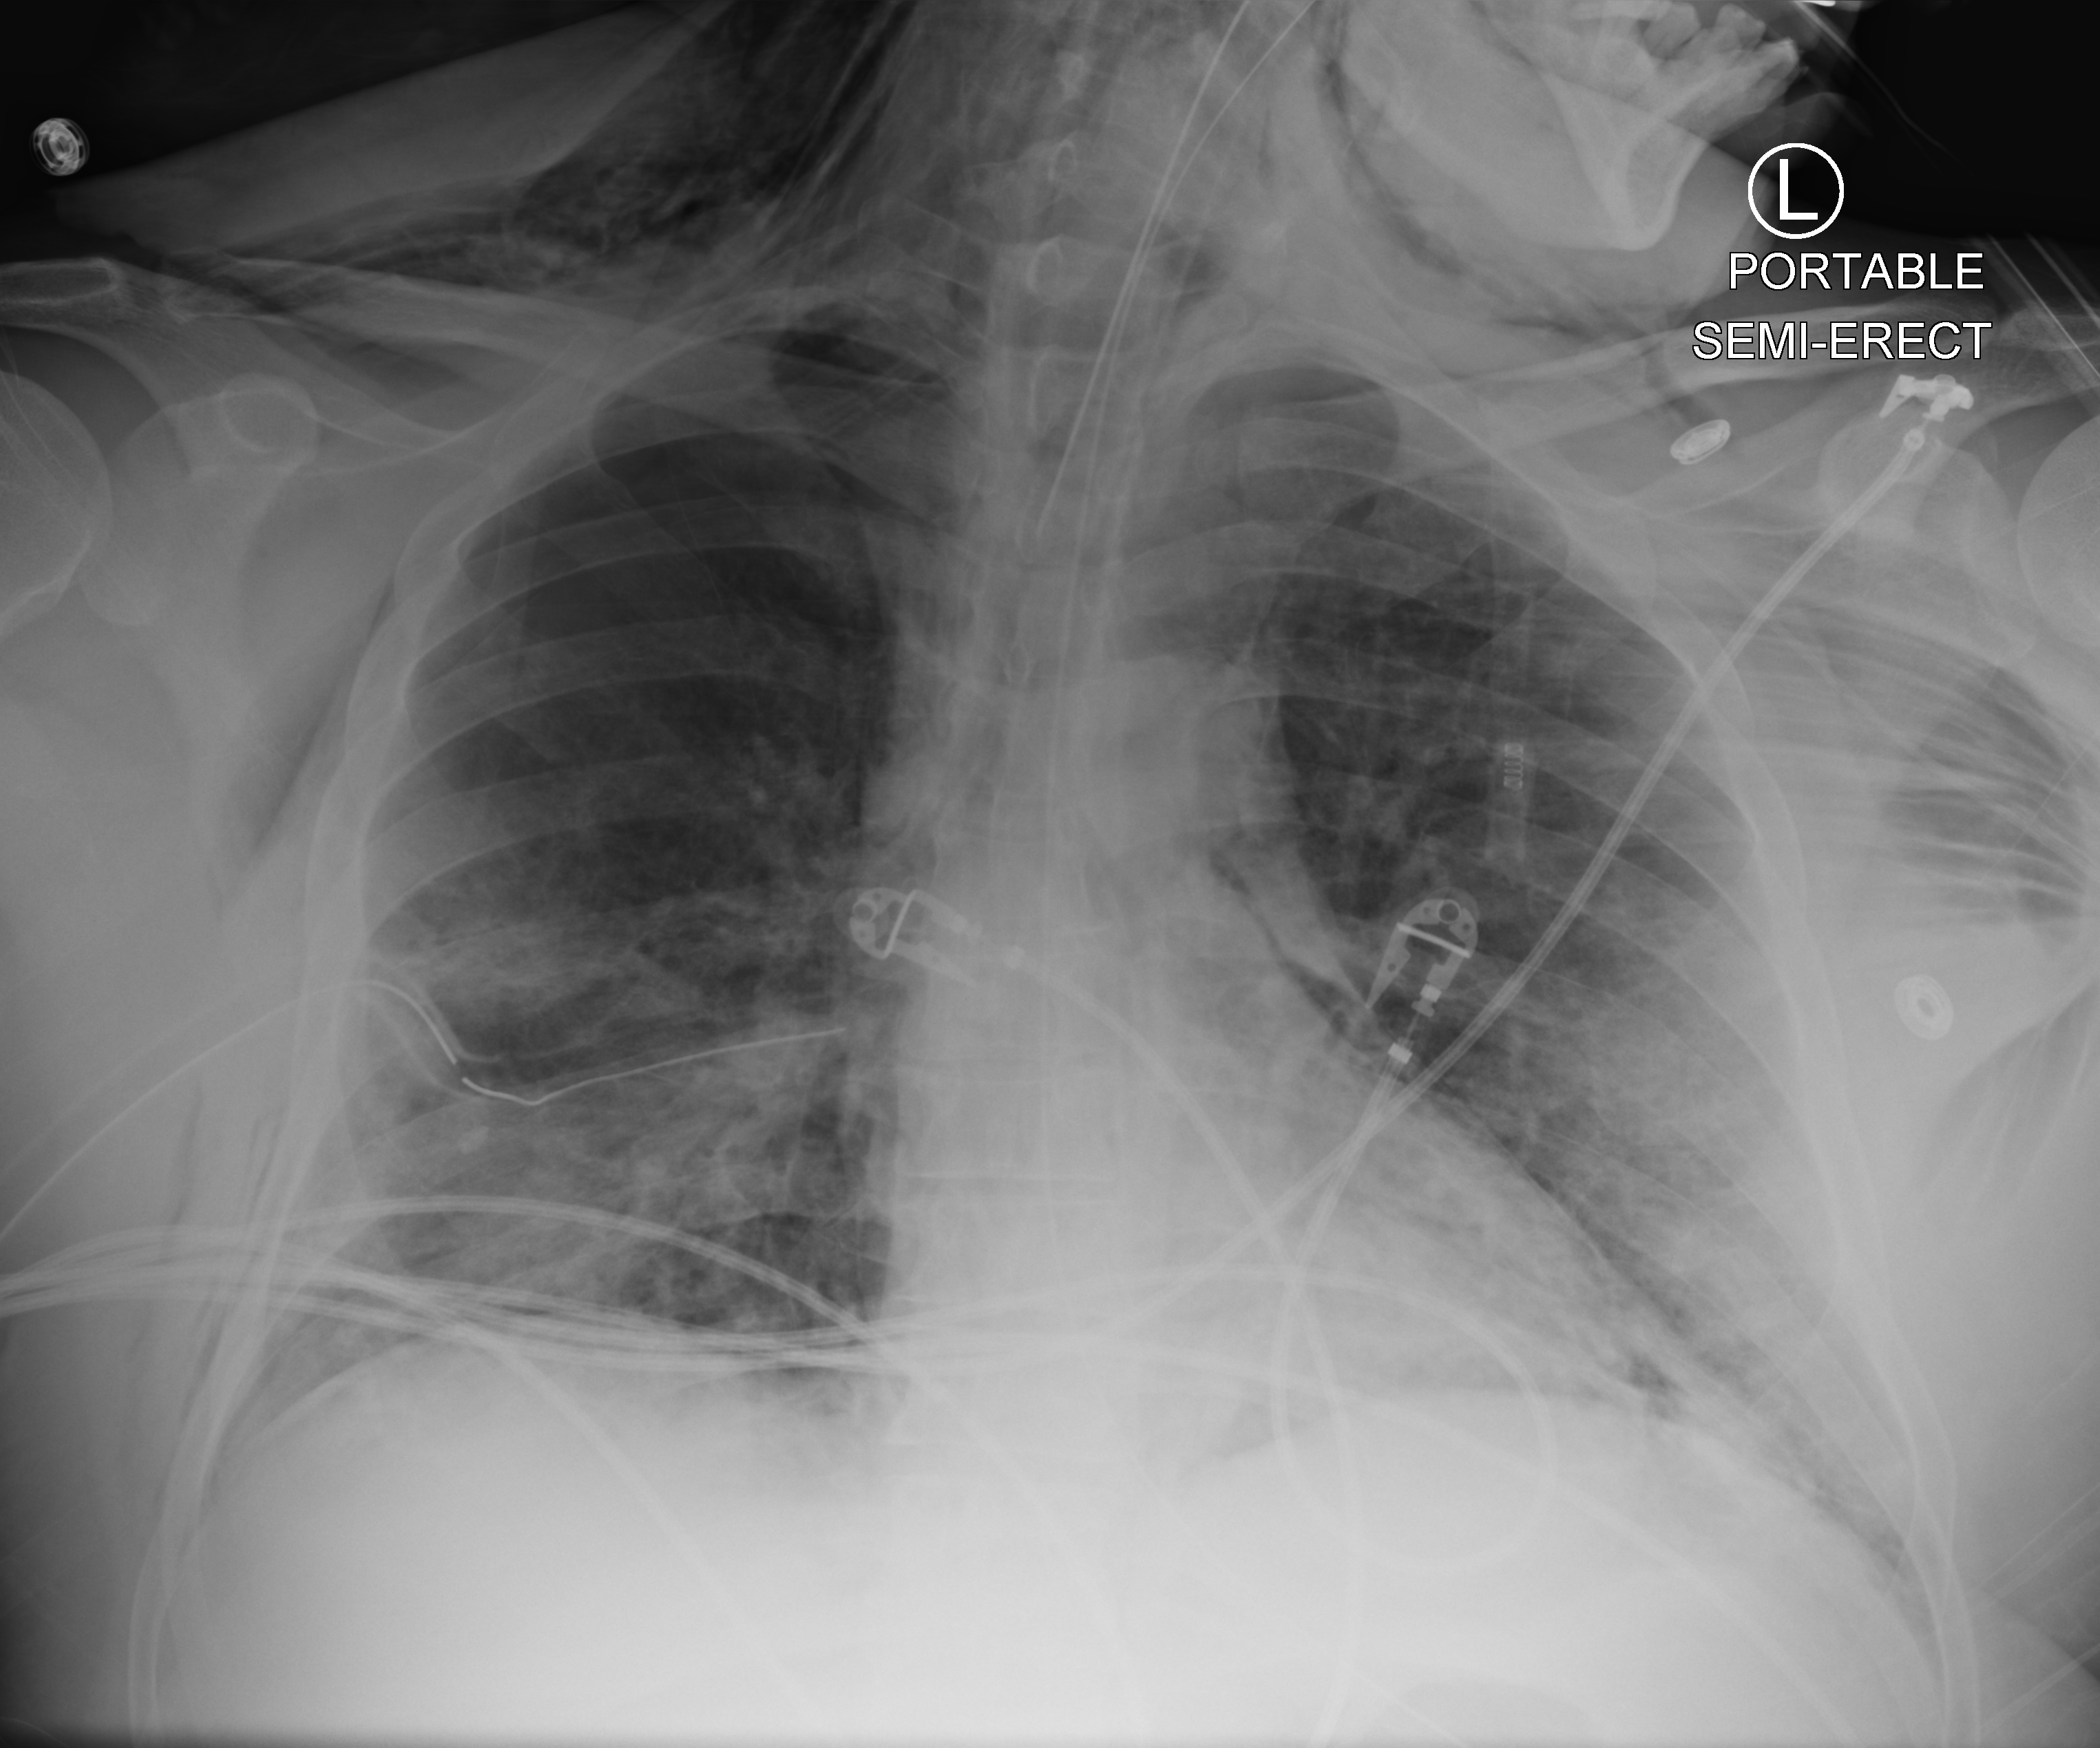
Portable chest radiograph, anteroposterior (AP) projection. Patient hospitalised with COVID-19; male, aged 18–59 years.
Hospital-stay facts (about this admission, not read from this image; timing relative to this image not recorded): smoking status (admission record): never.